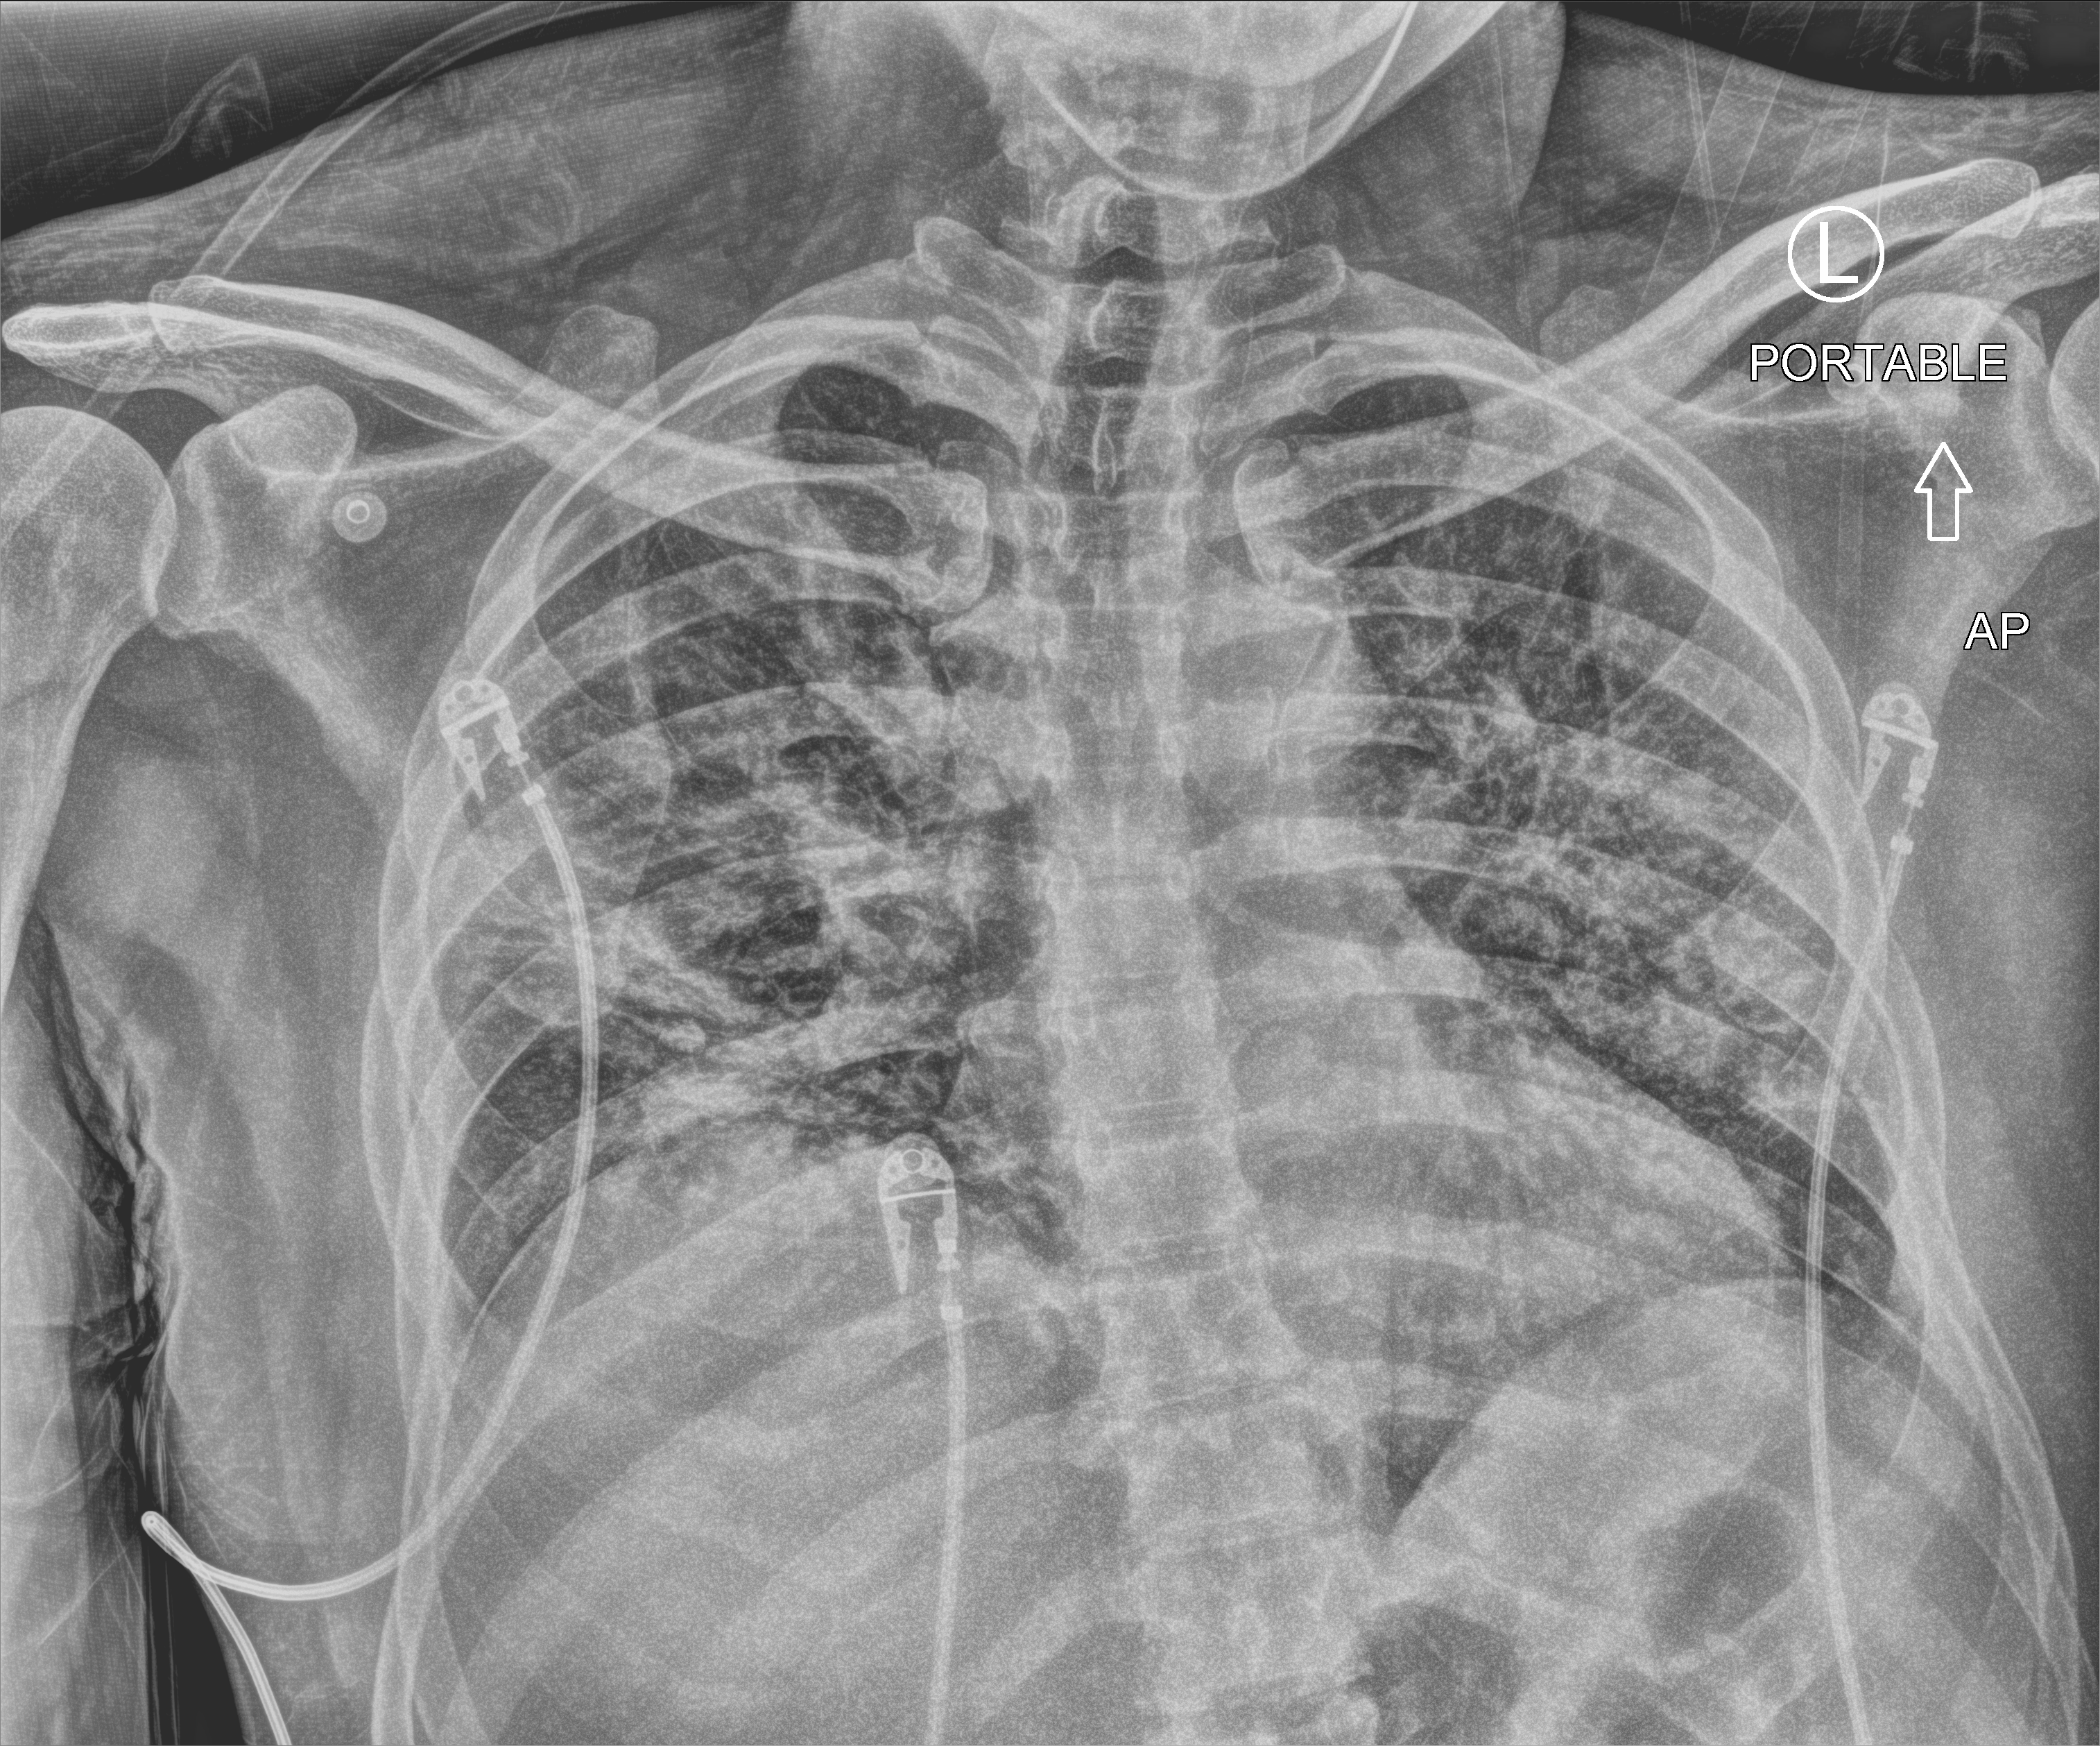
Portable chest radiograph; anteroposterior (AP) projection. Patient hospitalised with COVID-19; male, aged 18–59 years.
Admission-level facts for this patient (not findings on this image; timing relative to this image not recorded): diabetes (admission record): no; admitted to intensive care during this hospital stay: no.